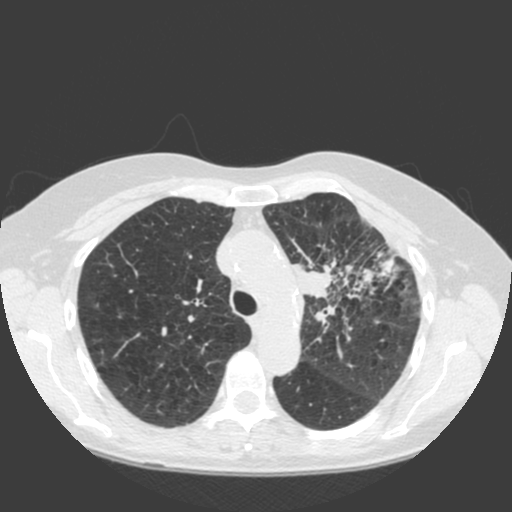
Low-dose screening chest CT, axial slice. First (baseline) screen. Lung window (W 1500 / L -600 HU). Standard (soft-tissue) reconstruction kernel (C). Slice 47 of 184 in the series. Female, age 66 years at enrolment.
Expert-annotated lung lesion, bounding box (x1, y1, x2, y2) in pixels: (286, 242, 397, 341). Reader record for this screening exam (exam-level; its link to the box is not recorded): non-calcified nodule or mass ≥4 mm, left upper lobe, 61 × 45 mm, spiculated (stellate) margins, soft tissue attenuation. Lung cancer was diagnosed 19 days after this screen: squamous cell carcinoma, keratinizing, NOS, left upper lobe, left hilum, mediastinum, left main stem bronchus, other location, poorly differentiated (G3), stage IIIB (AJCC 6th edition), 60 mm at pathology.